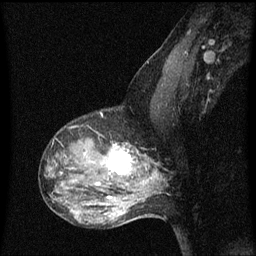
Breast MRI (dynamic contrast-enhanced), one sagittal slice; position 40 of 60 along the scan axis; dynamic contrast-enhanced series, image 2 of 3 at this slice position (ordered by acquisition); 1.5 T; TE 4.2 ms, TR 8 ms; 2 mm slice thickness; 256 × 256 image matrix. Patient: female, 50 years.
Outlined on this slice (semi-automatically segmented with operator editing):
- analysis volume of interest (the breast-tissue region the enhancement analysis was run in; not a lesion): bounding box <91,140,141,189> (left, top, right, bottom; pixels)
- tumour enhancement mask (voxels above the 70 % enhancement threshold inside the analysis volume of interest): <96,146,133,185>